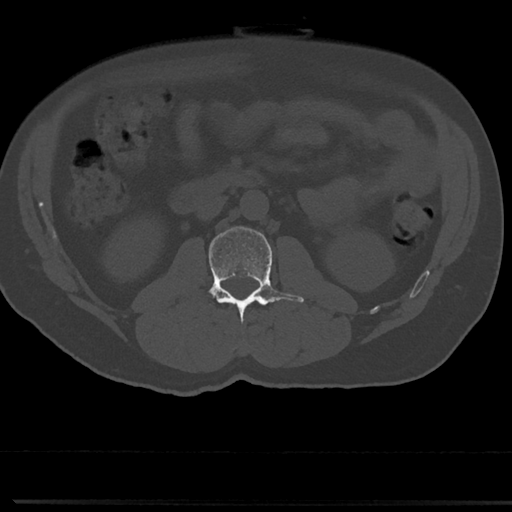
CT including the spine, one axial slice; slice 13 of 817 in the series (ordered by position); bone window (W 1800 / L 400 HU); 0.5 mm slice thickness; 512 × 512 image matrix. Male patient, age 61 years. Case-level facts recorded for this patient, not image findings: primary cancer: prostate.
Structures marked on this image (semi-automatic segmentation, software-assisted and operator-edited):
- L2 vertebra: box from (x=209, y=226) to (x=304, y=326) px